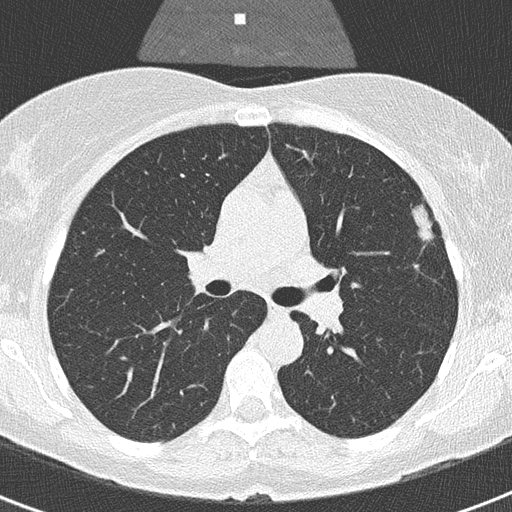
Chest CT (low-dose screening protocol), one axial image, second screening round (one year after baseline), lung window (W 1500 / L -600 HU), 2 mm slice thickness, lung (sharp) reconstruction kernel (B50f), 120 kVp. Female, age 56 years at enrolment.
- Expert-annotated lung lesion, bounding box (x1, y1, x2, y2) in pixels: (406, 201, 455, 255).
- Reader record for this screening exam (exam-level; its link to the box is not recorded): non-calcified nodule or mass ≥4 mm, left upper lobe, 20 × 9 mm, smooth margins, soft tissue attenuation, pre-existing on the prior screen: yes; interval growth: yes.
- Later outcome: lung cancer diagnosed 55 days after this screen — adenocarcinoma, NOS, left upper lobe, moderately differentiated (G2), stage IA (AJCC 6th edition), 11 mm at pathology.